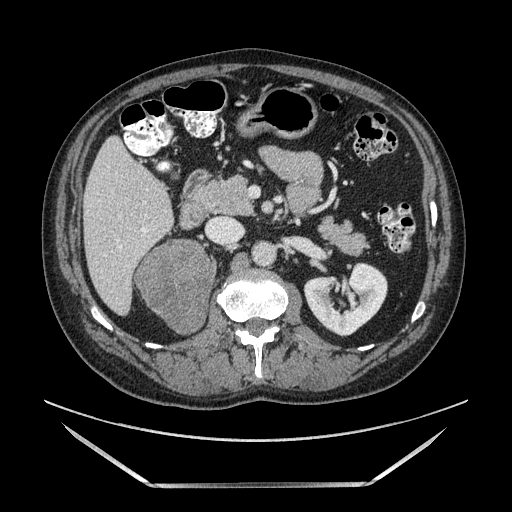
Contrast-enhanced abdominal CT, one axial slice. Position 61 of 185 along the scan axis. Soft-tissue window (W 400 / L 40 HU). 1.25 mm slice thickness. 512 × 512 image matrix, field of view 440 × 440 mm. Male patient. From the clinical record (not read from this slice): diagnosis: adrenocortical carcinoma; tumour side: right adrenal; tumour size at pathology: 10.3 cm; Ki-67 index: 20 %; stage (as recorded): 3.
Structures marked on this image (semi-automatic segmentation, software-assisted and operator-edited):
- mass: box from (x=138, y=241) to (x=213, y=332) px